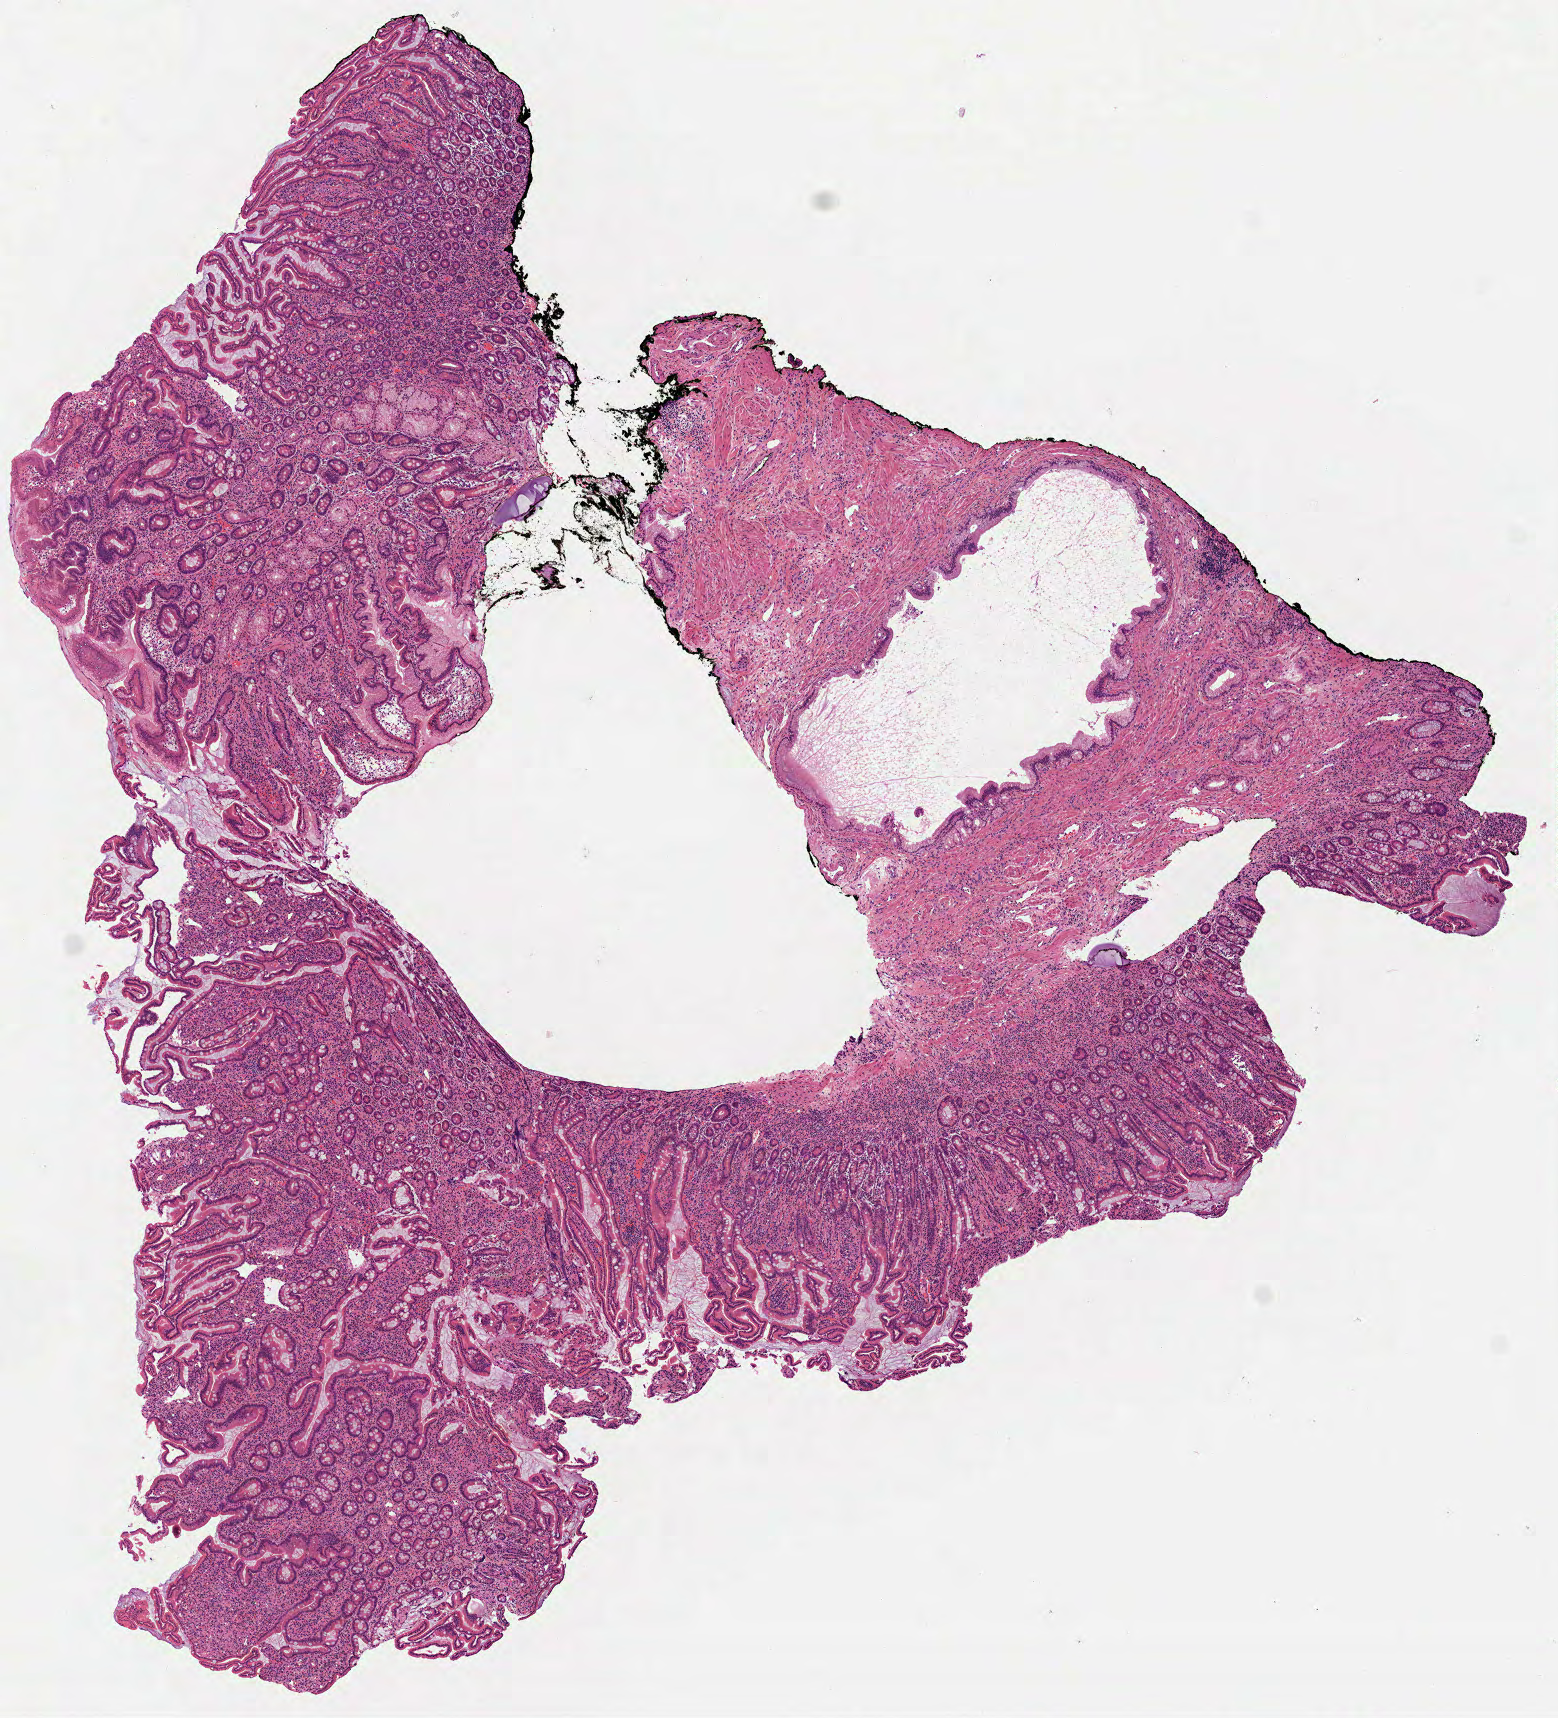
H&E-stained whole-slide image — low-resolution overview of the scanned area, about 6.3 x 6.9 mm, formalin-fixed paraffin-embedded (FFPE) diagnostic section, sample: primary tumour, pancreas. Female patient; age at initial diagnosis 60 years. Histologic grade: G2 (moderately differentiated).
* AJCC pathologic stage: IIA (7th edition)
* lymph nodes positive (case pathology): 0 of 17 examined
* pathologic diagnosis: Infiltrating duct carcinoma, NOS (head of pancreas)